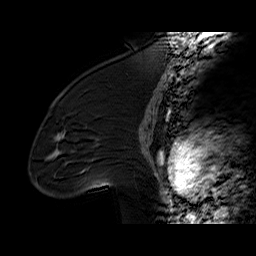
Breast MRI (dynamic contrast-enhanced), one sagittal slice; position 40 of 60 along the scan axis; dynamic contrast-enhanced series, time point 2 of 6 at this slice position (early post-contrast); 1.5 T; TE 6.2 ms, TR 32.4 ms; 256 × 256 image matrix, field of view 200 × 200 mm. Female patient. From the clinical record (not read from this slice): setting: breast cancer imaged before/during neoadjuvant chemotherapy; receptor status: triple-negative.
Annotated regions visible in this slice (semi-automatically segmented with operator editing):
- analysis volume of interest (the breast-tissue region the enhancement analysis was run in; not a lesion): bounding box <36,97,134,196> (left, top, right, bottom; pixels)
- tumour enhancement mask (voxels above the 100 % enhancement threshold inside the analysis volume of interest): <61,136,63,139>